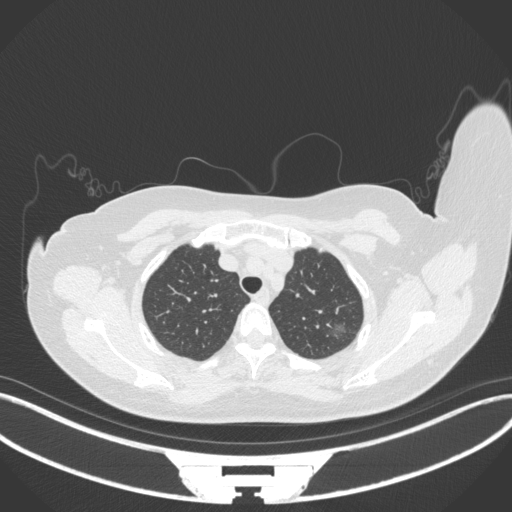
Chest CT, one axial slice. Slice 304 of 386 in the series (ordered by position). Reconstruction kernel B31f. 120 kVp. Lung window (W 1500 / L -600 HU). 1 mm slice thickness. 512 × 512 image matrix, field of view 400 × 400 mm. Patient: female, 58 years. From the clinical record (not read from this slice): clinical TNM (as recorded): T1c N0 M0.
Annotated regions visible in this slice (rectangle marked by the reading radiologist):
- lung tumour (recorded histology: adenocarcinoma): bounding box <323,316,350,343> (left, top, right, bottom; pixels)